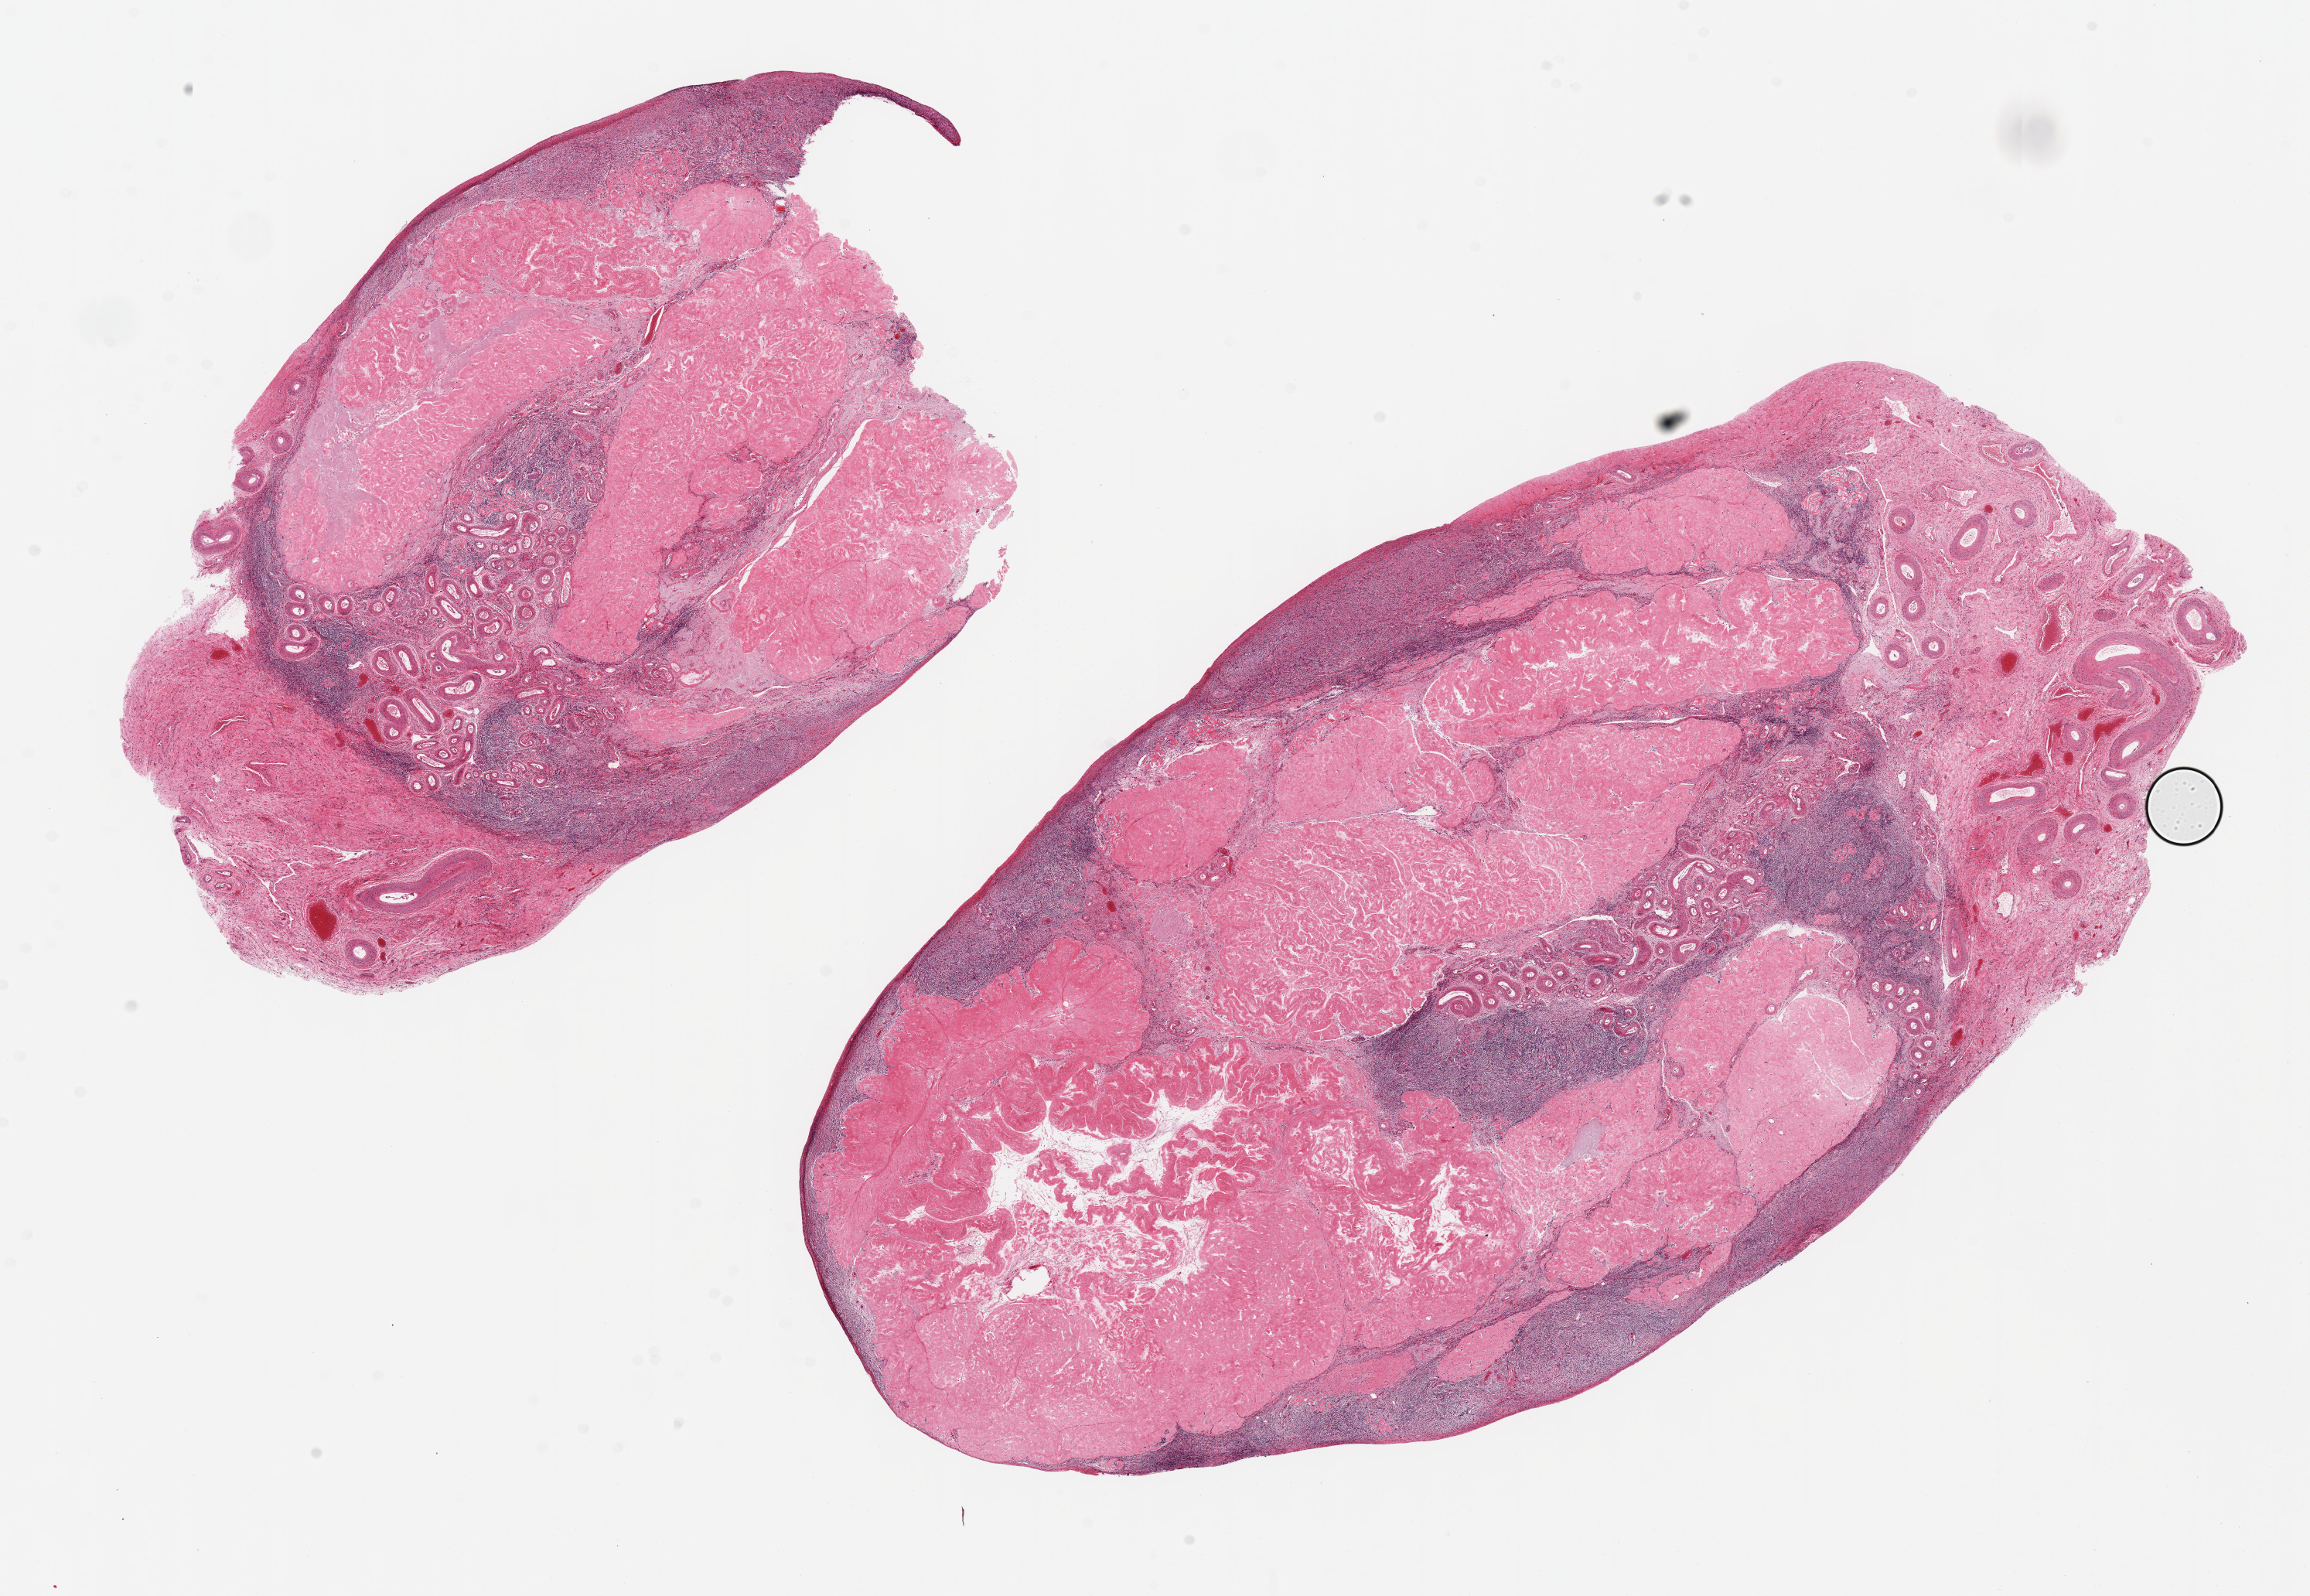
Digitized hematoxylin and eosin (H&E)-stained section, brightfield, a low-resolution overview of the entire scanned area, about 23.6 x 16.3 mm (from a 20x scan), PAXgene-fixed, paraffin-embedded tissue, section of ovary (target tissue), tissue donor sample. Female donor.
Review note (as recorded): 2 ~12x7.5mm aliquots. Typical involuted/post-menopausal appearance; ~70% corpora albicantia.